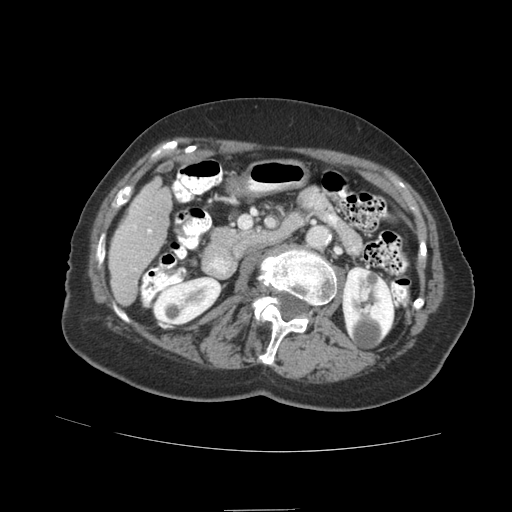
Contrast-enhanced abdominal CT (liver protocol), one axial slice. Position 26 of 89 along the scan axis. Reconstruction kernel STANDARD. 140 kVp. Soft-tissue window (W 400 / L 40 HU). 2.5 mm slice thickness. 512 × 512 image matrix, field of view 360 × 360 mm. Case-level facts recorded for this patient, not image findings: diagnosis: hepatocellular carcinoma (patient treated with transarterial chemoembolisation; whether this scan precedes or follows treatment is not stated here); TNM stage (as recorded): Stage-II; Child-Pugh class: A; tumour size: 4 cm.
Annotated regions visible in this slice (semi-automatic segmentation, software-assisted and operator-edited):
- liver parenchyma outside the tumour (the mass and vessels are separate outlines, so this box may not span the whole liver): bounding box <108,178,172,304> (left, top, right, bottom; pixels)
- liver vessels: <133,225,151,234>